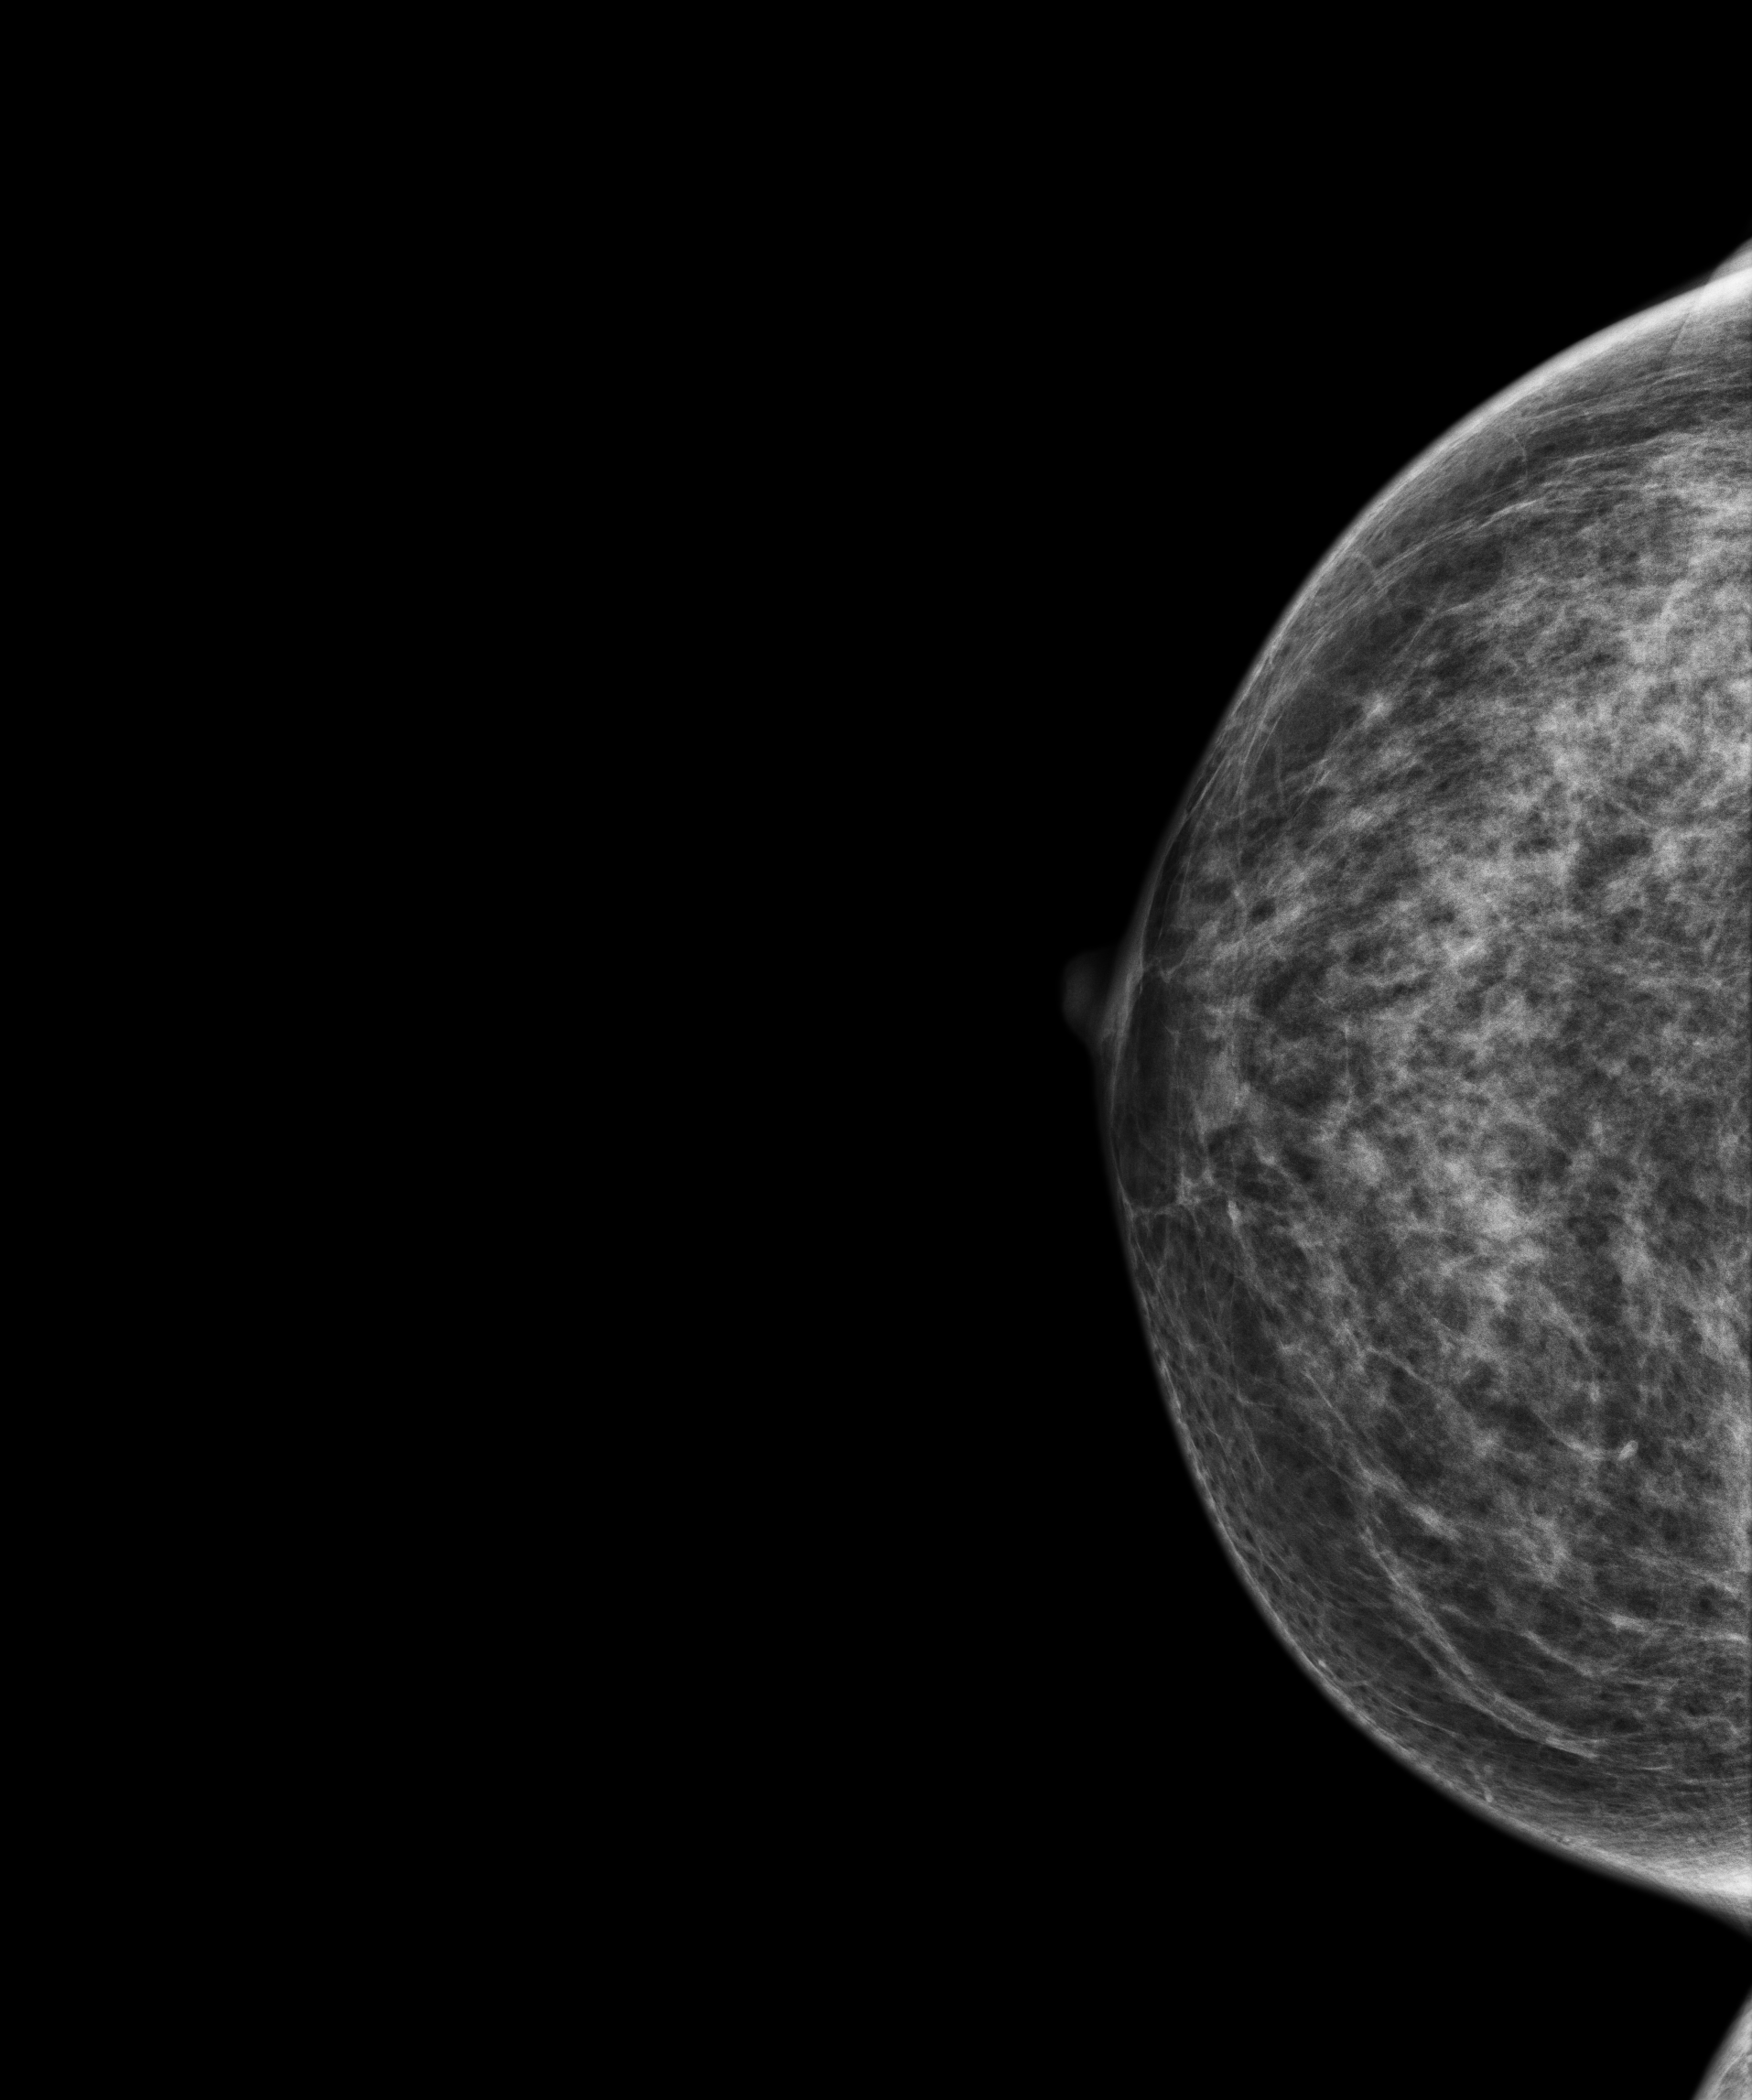
Screening examination, system: Senographe Essential ADS_56.21.3. Patient: female, 70 years.
Image type: full-field digital mammogram. Breast: right. Projection: craniocaudal (CC) view.